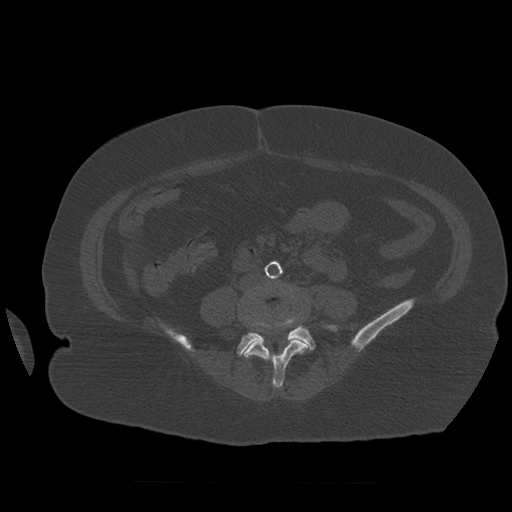
CT including the spine, one axial slice. Slice 195 of 399 in the series (ordered by position). Reconstruction kernel STANDARD. 120 kVp. Bone window (W 1800 / L 400 HU). 1.25 mm slice thickness. 512 × 512 image matrix, field of view 404 × 404 mm. Patient age 81 years. Case-level facts recorded for this patient, not image findings: primary cancer: renal.
Annotated regions visible in this slice (semi-automatic segmentation, software-assisted and operator-edited):
- L4 vertebra: bounding box <244,284,310,389> (left, top, right, bottom; pixels)
- L5 vertebra: <237,322,337,356>